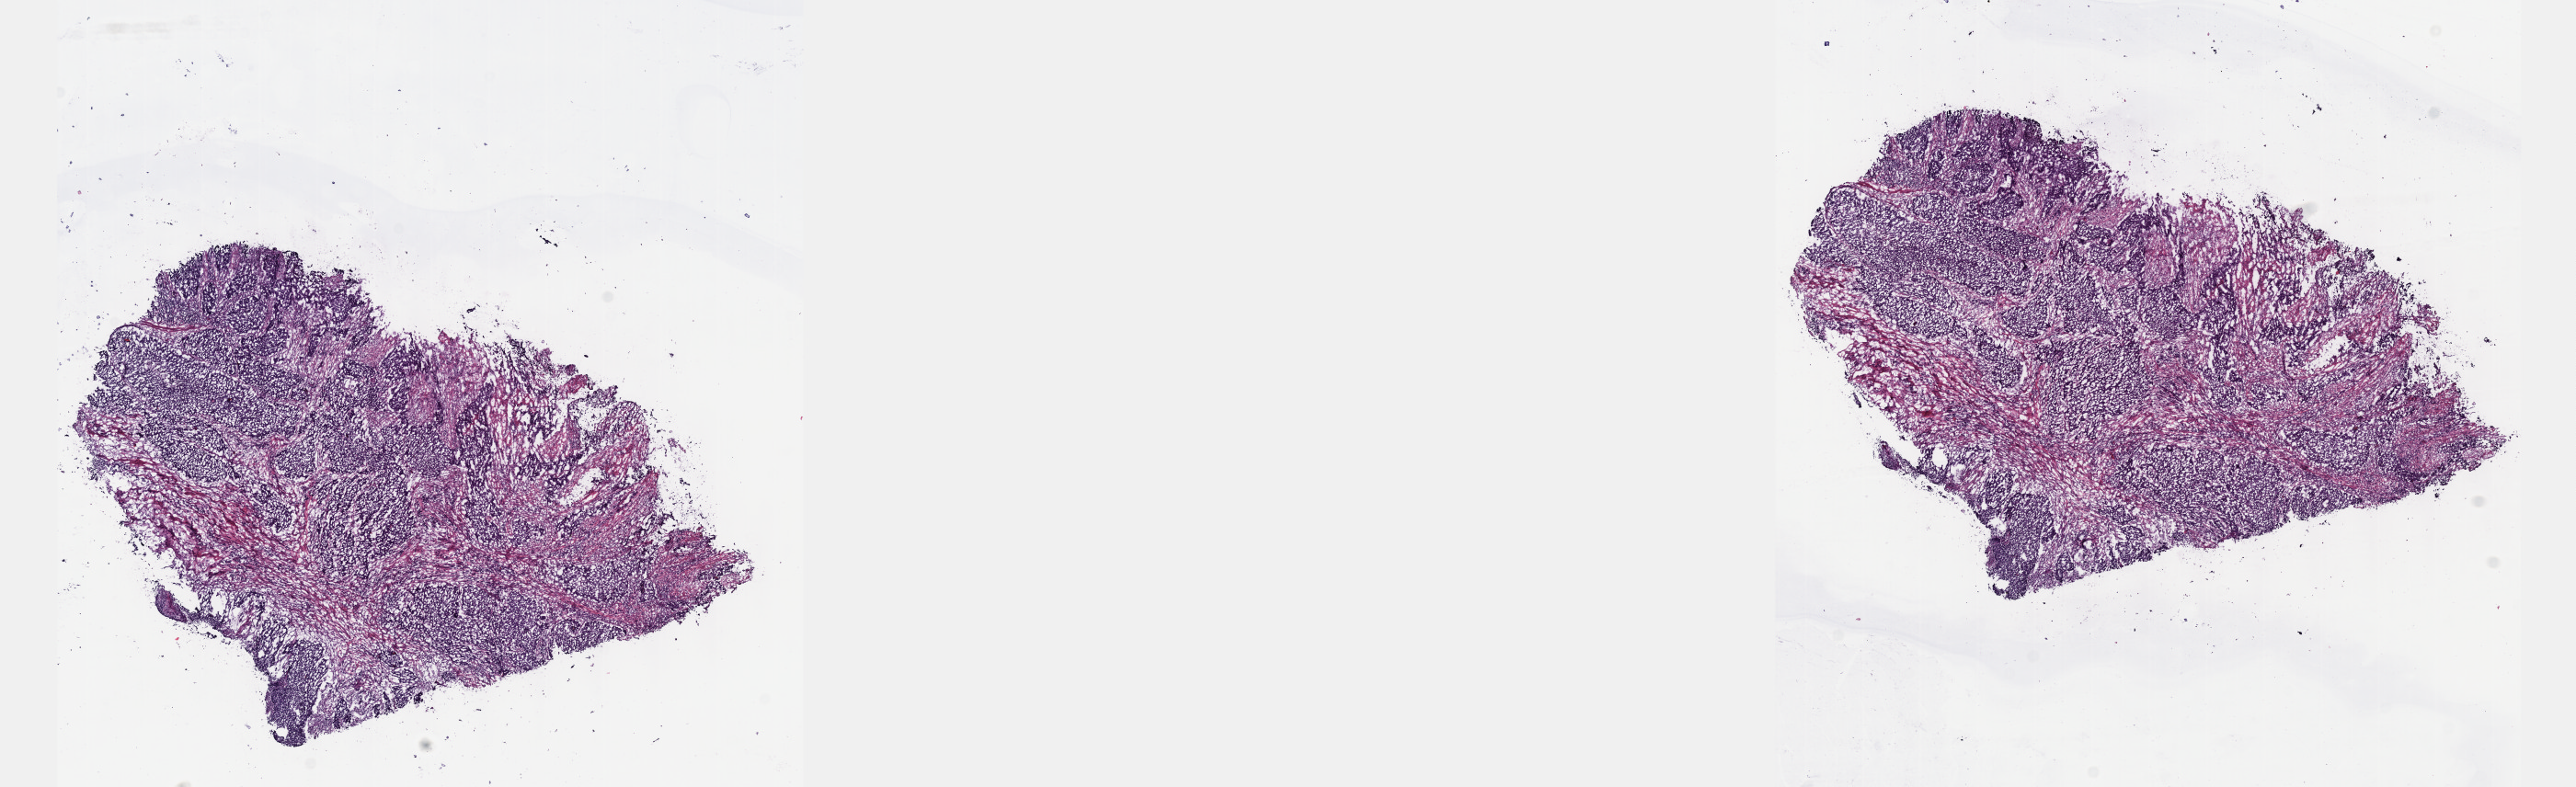
H&E whole-slide image — a low-resolution overview of the entire scanned area, about 22.6 x 6.9 mm (from a 40x scan). Frozen section from the top of the tissue portion. Esophagus, primary tumour sample. Male patient; age at initial diagnosis 49 years. Histologic grade: G2 (moderately differentiated). Composition of this section per pathologist review: tumour cells 100%, tumour nuclei 65%, normal cells 0%, stromal cells 0%, necrosis 0%. Infiltration values recorded for this section: lymphocyte infiltration 5%, monocyte infiltration 0%, neutrophil infiltration 0%.
• AJCC pathologic stage: IIA
• pathologic diagnosis: Squamous cell carcinoma, NOS (upper third of esophagus)